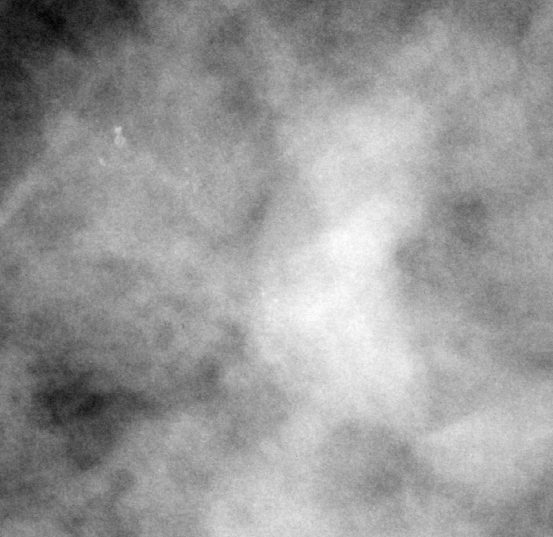
Crop from a digitized film mammogram around one marked abnormality, left breast, MLO view, BI-RADS breast density category 3 (scale 1–4).
- Marked abnormality: calcifications, morphology punctate, distribution segmental; BI-RADS assessment category 2; subtlety rating 1 on a 1 (subtle) to 5 (obvious) scale; pathology (as recorded): benign.